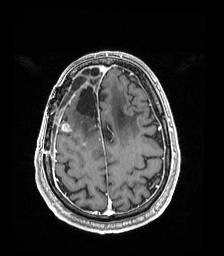
Brain MRI from a brain-tumour surgery series, one axial slice; slice 50 of 192 in the series (ordered by position); T1-weighted post-contrast; 1 mm slice thickness; 224 × 256 image matrix, field of view 224 × 256 mm. Case-level facts recorded for this patient, not image findings: histopathology: Astrocytoma; WHO grade: 4; IDH mutation: yes; tumour location: Right Frontal.
Outlined on this slice (manually delineated by an expert):
- previous resection cavity: bounding box <76,86,98,121> (left, top, right, bottom; pixels)